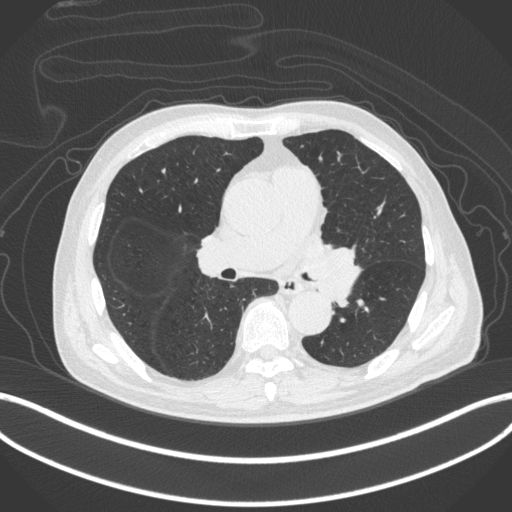
Chest CT, one axial slice. Position 238 of 420 along the scan axis. Reconstruction kernel B31f. Lung window (W 1500 / L -600 HU). 1 mm slice thickness. 512 × 512 image matrix. Male patient, age 77 years. Case-level facts recorded for this patient, not image findings: clinical TNM (as recorded): T3 N1 M0.
Outlined on this slice (bounding box drawn by a radiologist):
- lung tumour (recorded histology: adenocarcinoma): bounding box [x1, y1, x2, y2] px = [302, 239, 360, 304]